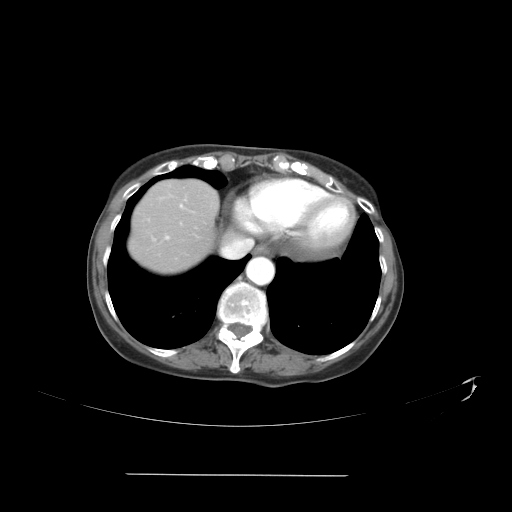
Contrast-enhanced abdominal CT, one axial slice; position 35 of 41 along the scan axis; reconstruction kernel STANDARD; 120 kVp; intravenous contrast given; soft-tissue window (W 400 / L 40 HU); 5 mm slice thickness; 512 × 512 image matrix, field of view 431 × 431 mm. Female patient, age 74 years. Case-level facts recorded for this patient, not image findings: diagnosis: colorectal cancer liver metastases, imaged before liver resection; multiple liver metastases: yes; largest metastasis: 3.3 cm; chemotherapy before resection: yes.
Annotated regions visible in this slice (expert manual segmentation):
- liver: bounding box (x1, y1, x2, y2) in pixels: (131, 181, 217, 272)
- planned liver remnant (the part of the liver to remain after resection): (133, 181, 217, 252)
- portal vein (with intrahepatic branches): (166, 205, 183, 240)